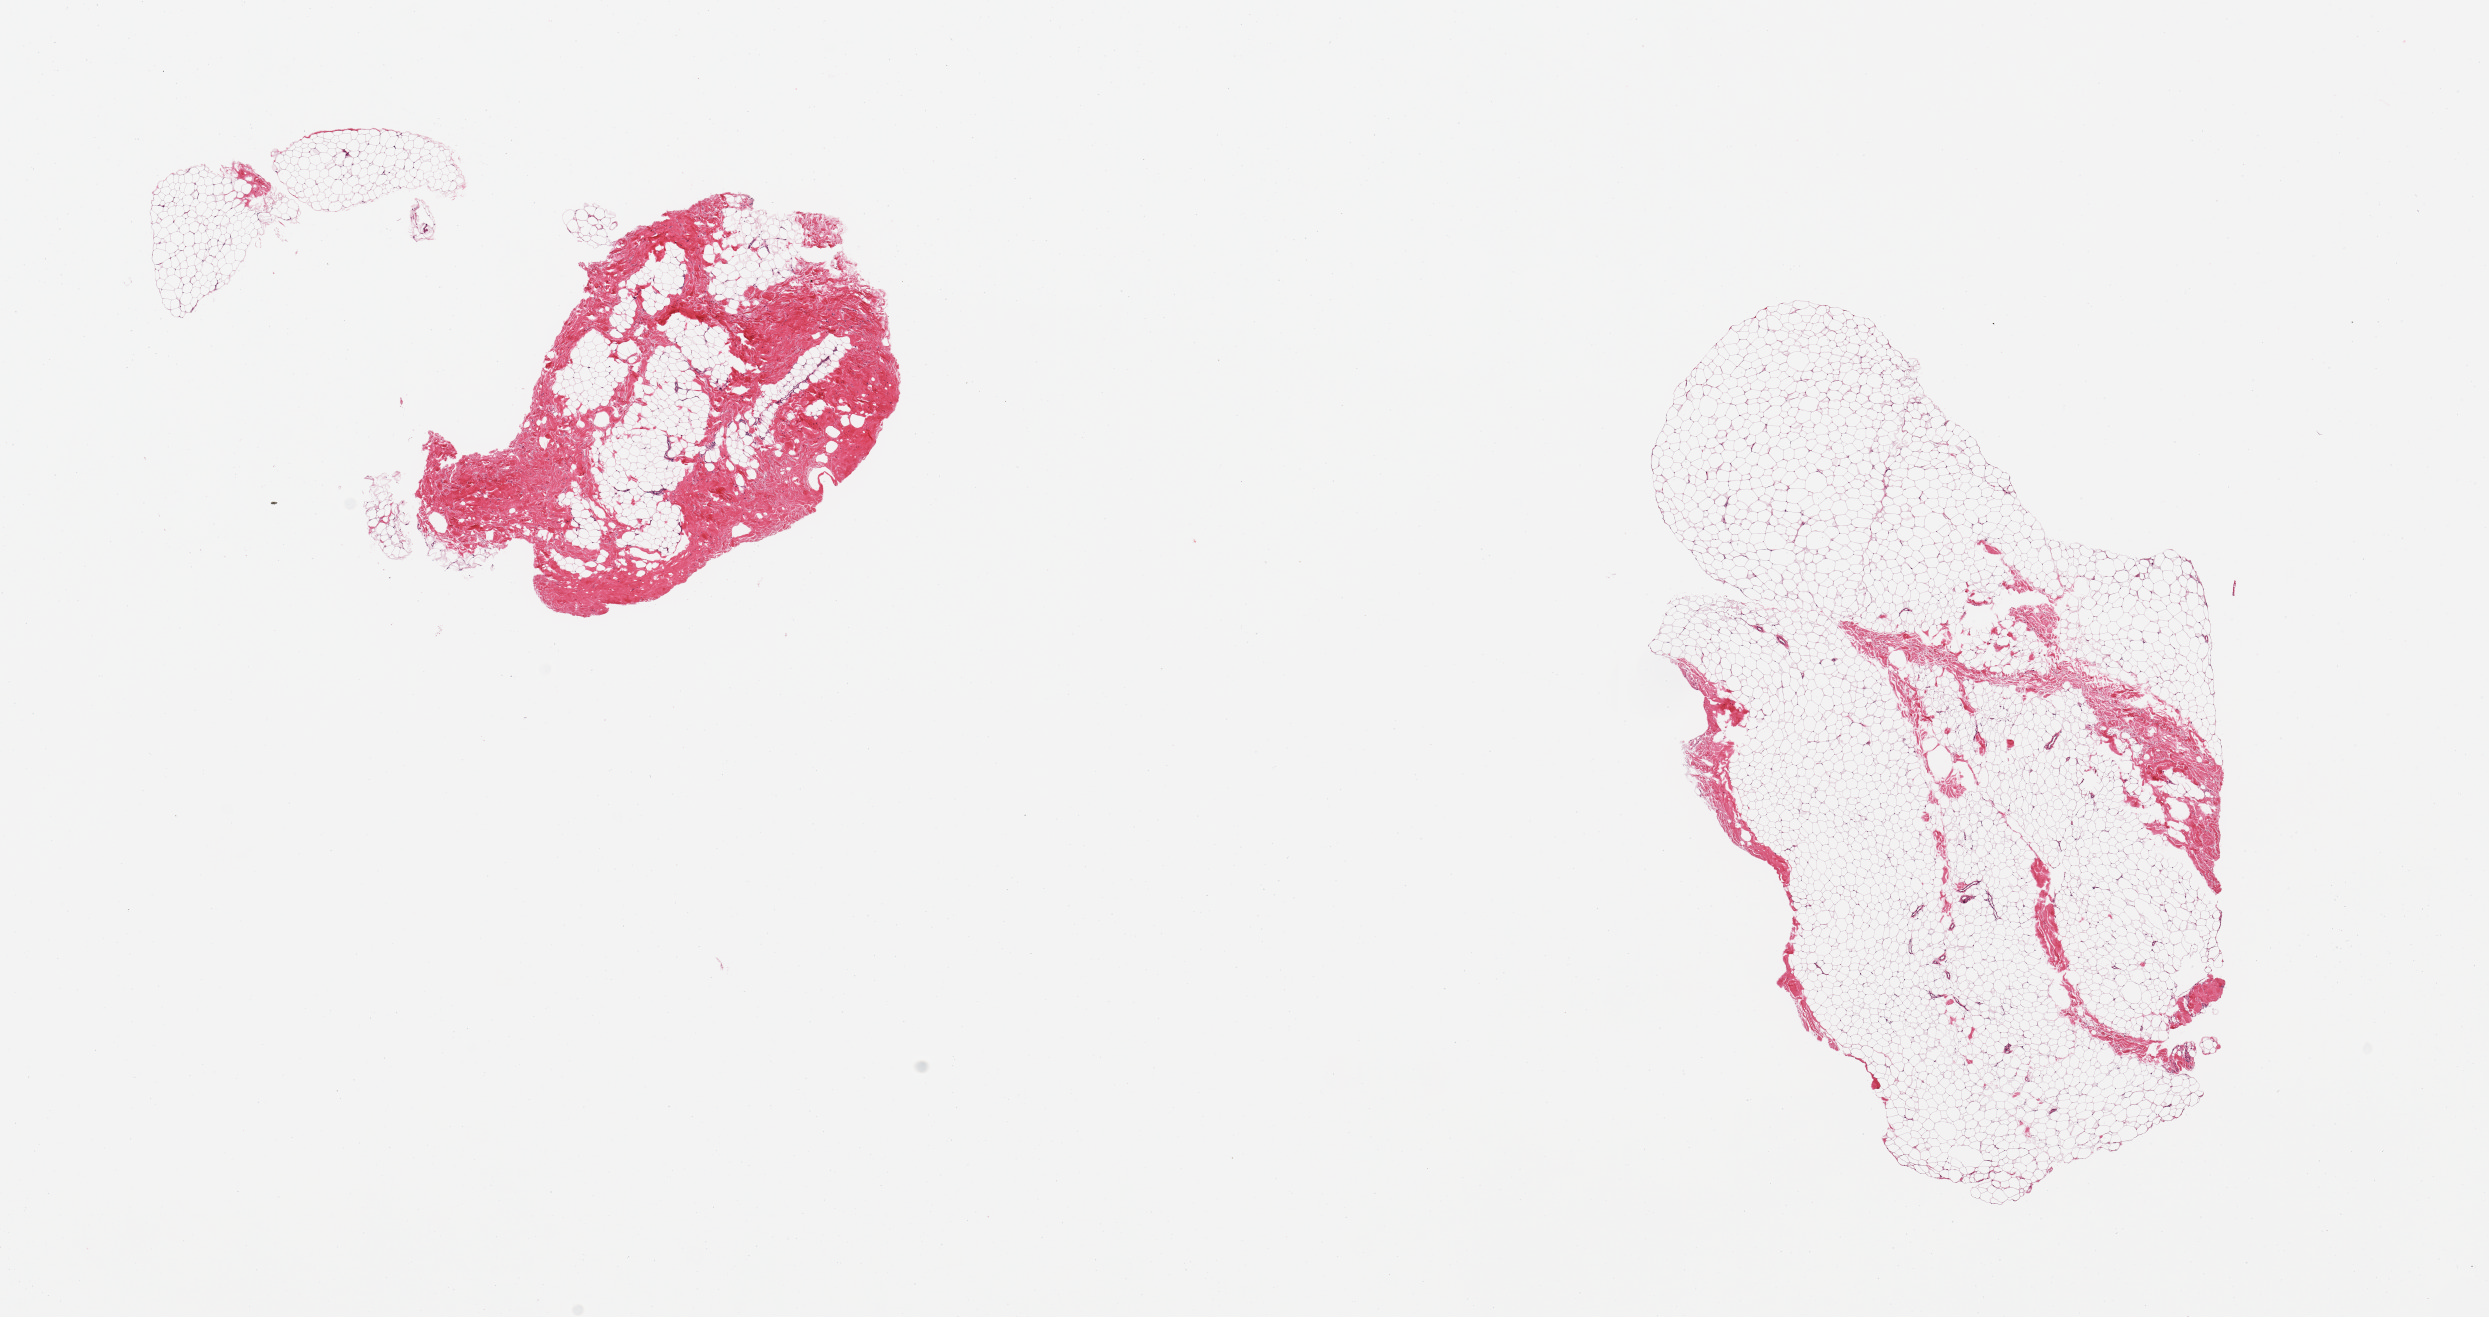
H&E whole-slide image, low-resolution overview of the scanned area, about 19.7 x 10.4 mm; PAXgene-fixed paraffin-embedded (PFPE) section; section of breast (target tissue); tissue donor sample. Male donor.
Reviewer comment on this tissue sample: 2 pieces; fibroadipose tissue without ducts.